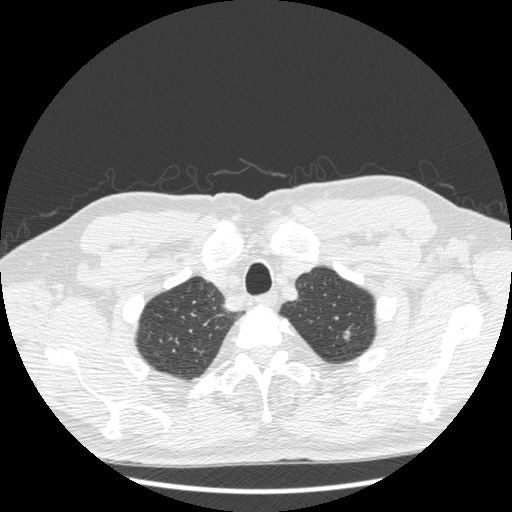
Low-dose screening chest CT, one axial slice; slice 193 of 223 in the series (ordered by position); 120 kVp; lung window (W 1500 / L -600 HU); 1.25 mm slice thickness; 512 × 512 image matrix.
Annotated regions visible in this slice (manually delineated by an expert):
- lesion 1 (tumor, upper lobe of left lung): box from (x=343, y=327) to (x=351, y=341) px